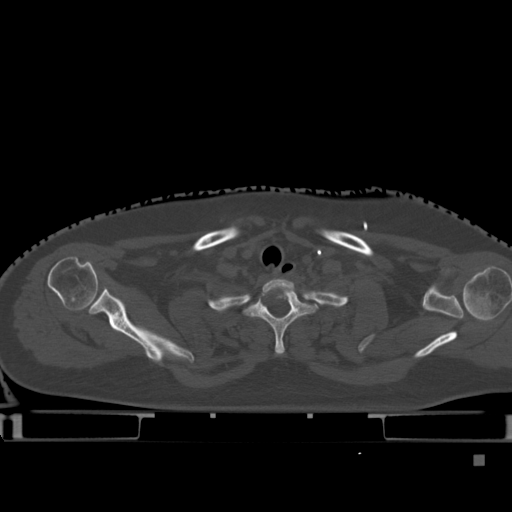
CT including the spine, one axial slice. Position 371 of 495 along the scan axis. Bone window (W 1800 / L 400 HU). 512 × 512 image matrix, field of view 404 × 404 mm. Female patient, age 33 years. Case-level facts recorded for this patient, not image findings: primary cancer: breast; vertebrae with lytic lesions (as recorded): T1.
Structures marked on this image (semi-automatically segmented with operator editing):
- T1 vertebra: box from (x=246, y=285) to (x=316, y=355) px